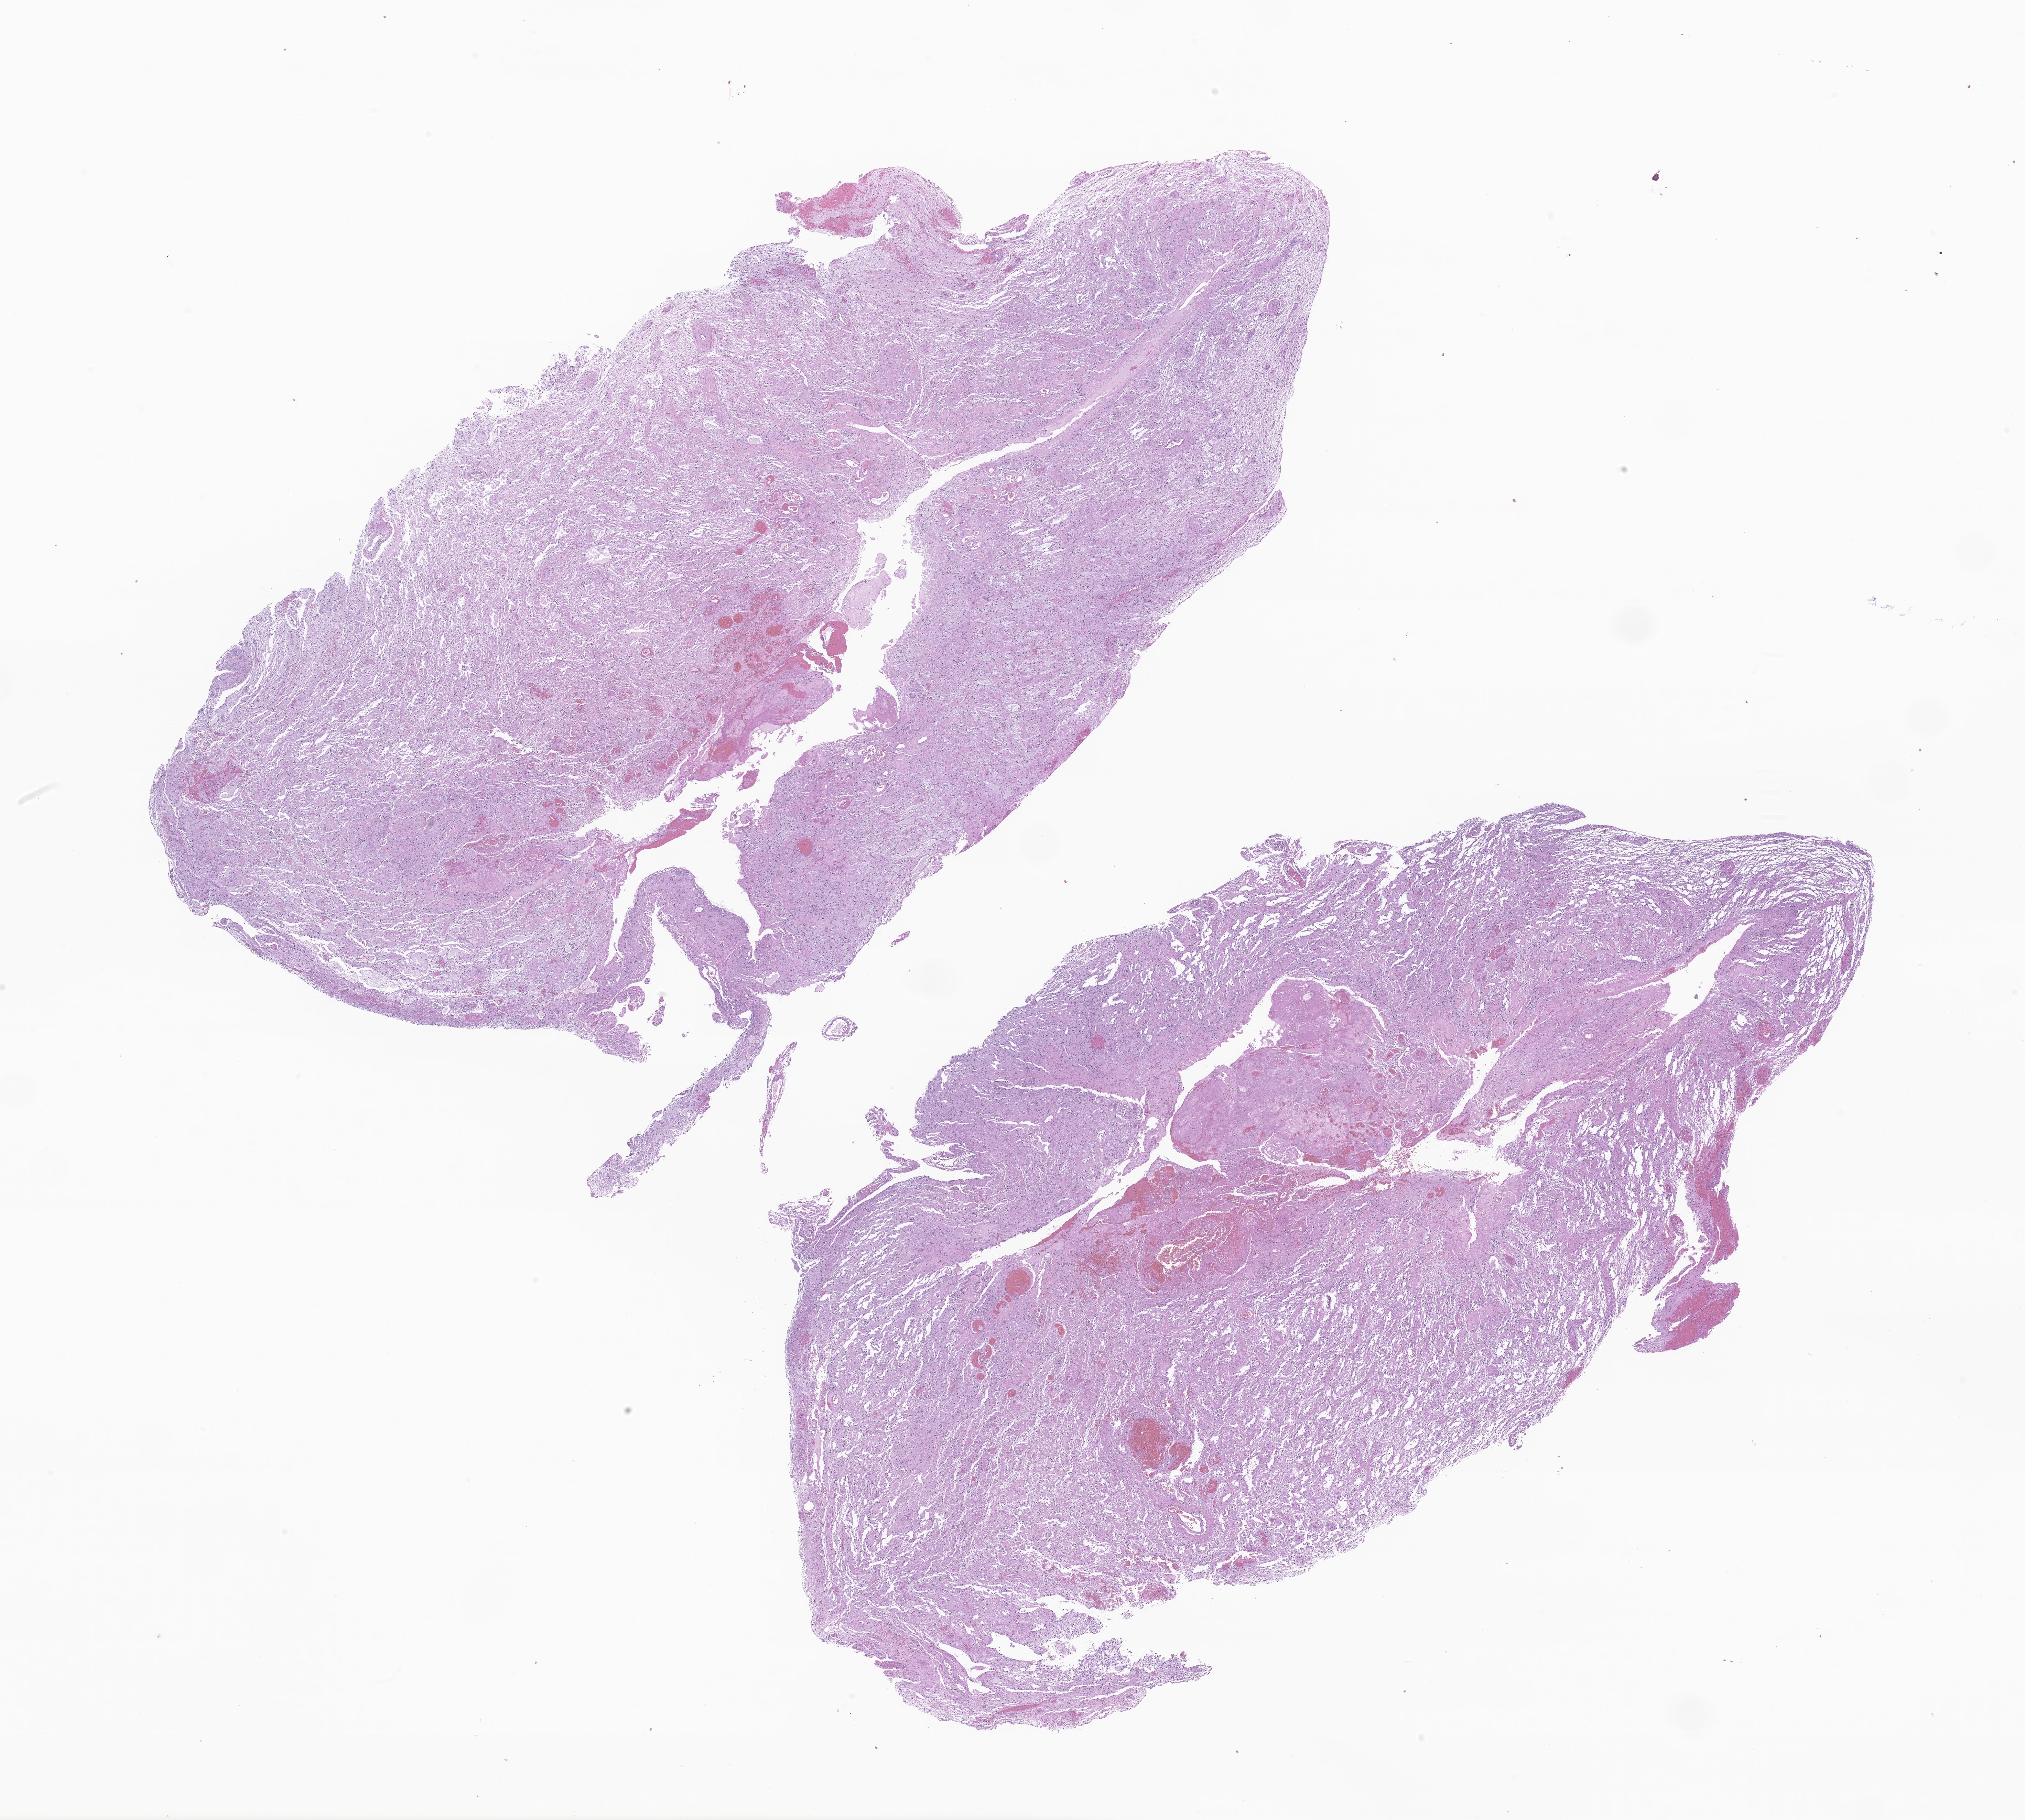
Whole-slide image, H&E stain of tumor tissue from the cerebellum — a low-resolution overview of the entire scanned area, about 24.8 x 22.3 mm, formalin-fixed paraffin-embedded section. Patient male; age 210 months (17 years 6 months).
* diagnosis: Pilocytic astrocytoma